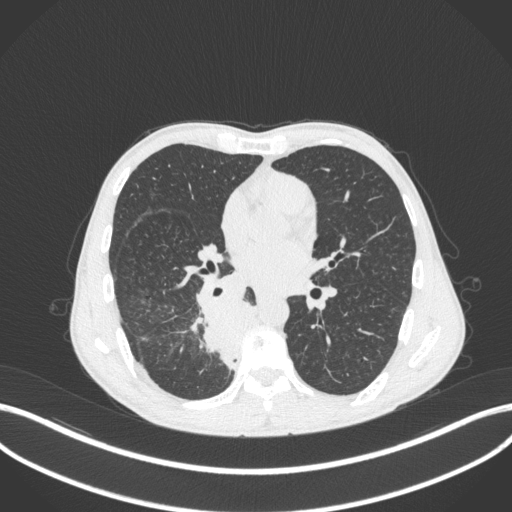
Chest CT, one axial slice. Position 187 of 371 along the scan axis. Reconstruction kernel B31f. Lung window (W 1500 / L -600 HU). 512 × 512 image matrix, field of view 400 × 400 mm. Patient: male, 58 years. Case-level facts recorded for this patient, not image findings: clinical TNM (as recorded): T3 N1 M1.
Outlined on this slice (rectangle marked by the reading radiologist):
- lung tumour (recorded histology: squamous cell carcinoma): box from (x=181, y=300) to (x=262, y=371) px